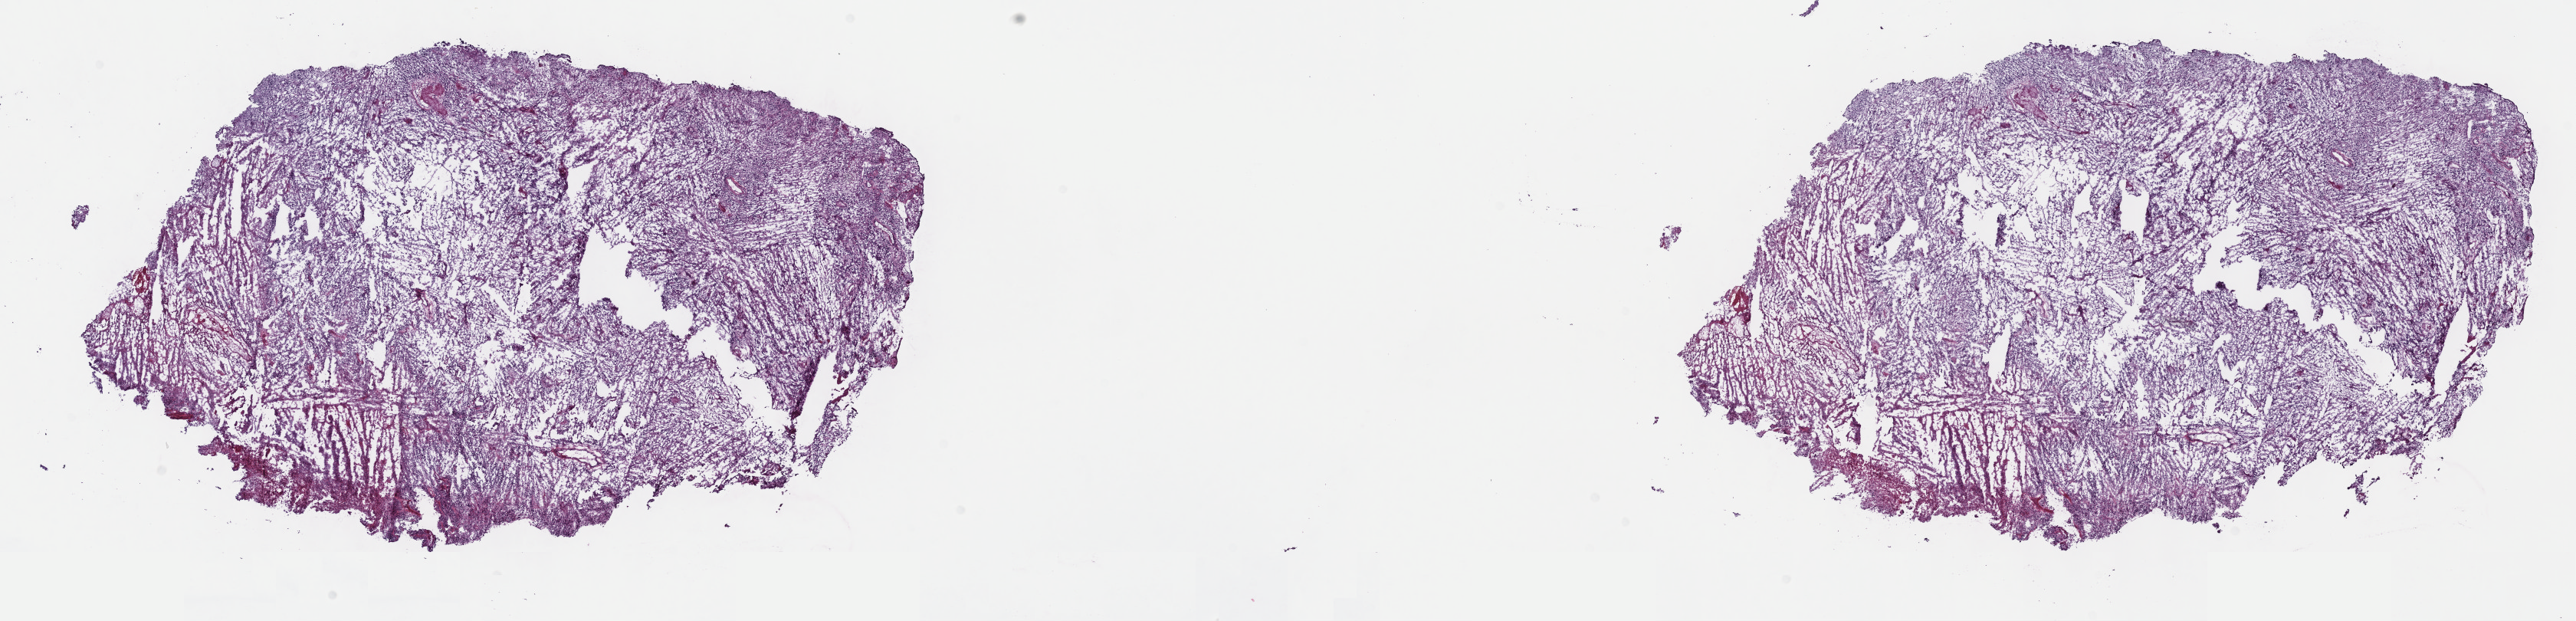
Hematoxylin and eosin (H&E) stained whole-slide image, whole scanned area (about 27.2 x 6.6 mm, slide scanned at 40x) shown as a low-resolution overview. Frozen section from the top of the tissue portion. Brain, primary tumour sample. Male, age 69 years at initial diagnosis. Composition of this section per pathologist review: tumour cells 40%, tumour nuclei 90%, normal cells 5%, stromal cells 25%, necrosis 30%. Infiltration values recorded for this section: lymphocyte infiltration 2%, monocyte infiltration 0%, neutrophil infiltration 0%.
Diagnosis: Glioblastoma.